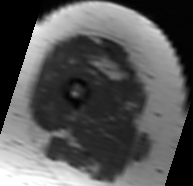
MRI of an extremity soft-tissue mass, one axial slice. Position 19 of 91 along the scan axis. MR volume resampled by the dataset authors to the PET/CT grid (not the native acquisition matrix). 3.27 mm slice thickness. 193 × 186 image matrix, field of view 188 × 182 mm. Female patient. From the clinical record (not read from this slice): histological type: malignant solitary fibrous tumor; grade: intermediate; site of the primary tumour: right thigh.
Structures marked on this image (expert contour drawn on MRI and transferred to this co-registered scan by the dataset authors):
- gross tumour volume including surrounding oedema: bounding box [x1, y1, x2, y2] px = [69, 37, 130, 82]